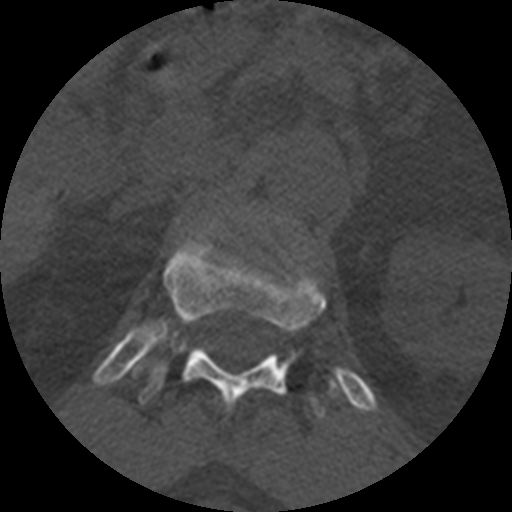
CT including the spine, one axial slice. Position 383 of 399 along the scan axis. Reconstruction kernel STANDARD. 120 kVp. Bone window (W 1800 / L 400 HU). 512 × 512 image matrix, field of view 160 × 160 mm. Patient age 71 years. Case-level facts recorded for this patient, not image findings: primary cancer: prostate.
Structures marked on this image (semi-automatic segmentation, software-assisted and operator-edited):
- T12 vertebra: box from (x=140, y=225) to (x=337, y=412) px